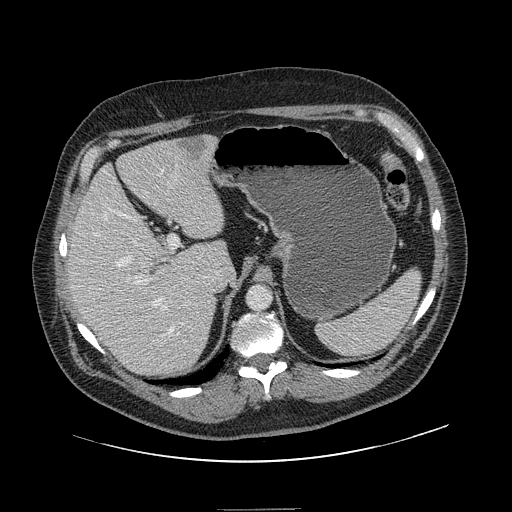
Contrast-enhanced abdominal CT, one axial slice. Slice 101 of 154 in the series (ordered by position). 120 kVp. Intravenous contrast given. Soft-tissue window (W 400 / L 40 HU). 2.5 mm slice thickness. 512 × 512 image matrix. Male patient, age 61 years. From the clinical record (not read from this slice): diagnosis: colorectal cancer liver metastases, imaged before liver resection; multiple liver metastases: yes; largest metastasis: 2.6 cm; disease in both lobes: yes.
Structures marked on this image (outlined manually by an expert reader):
- hepatic veins: box from (x=95, y=212) to (x=184, y=337) px
- liver: (x=68, y=136)–(x=225, y=379)
- planned liver remnant (the part of the liver to remain after resection): (x=68, y=144)–(x=226, y=361)
- portal vein (with intrahepatic branches): (x=108, y=169)–(x=185, y=305)
- liver metastasis: (x=178, y=138)–(x=206, y=162)